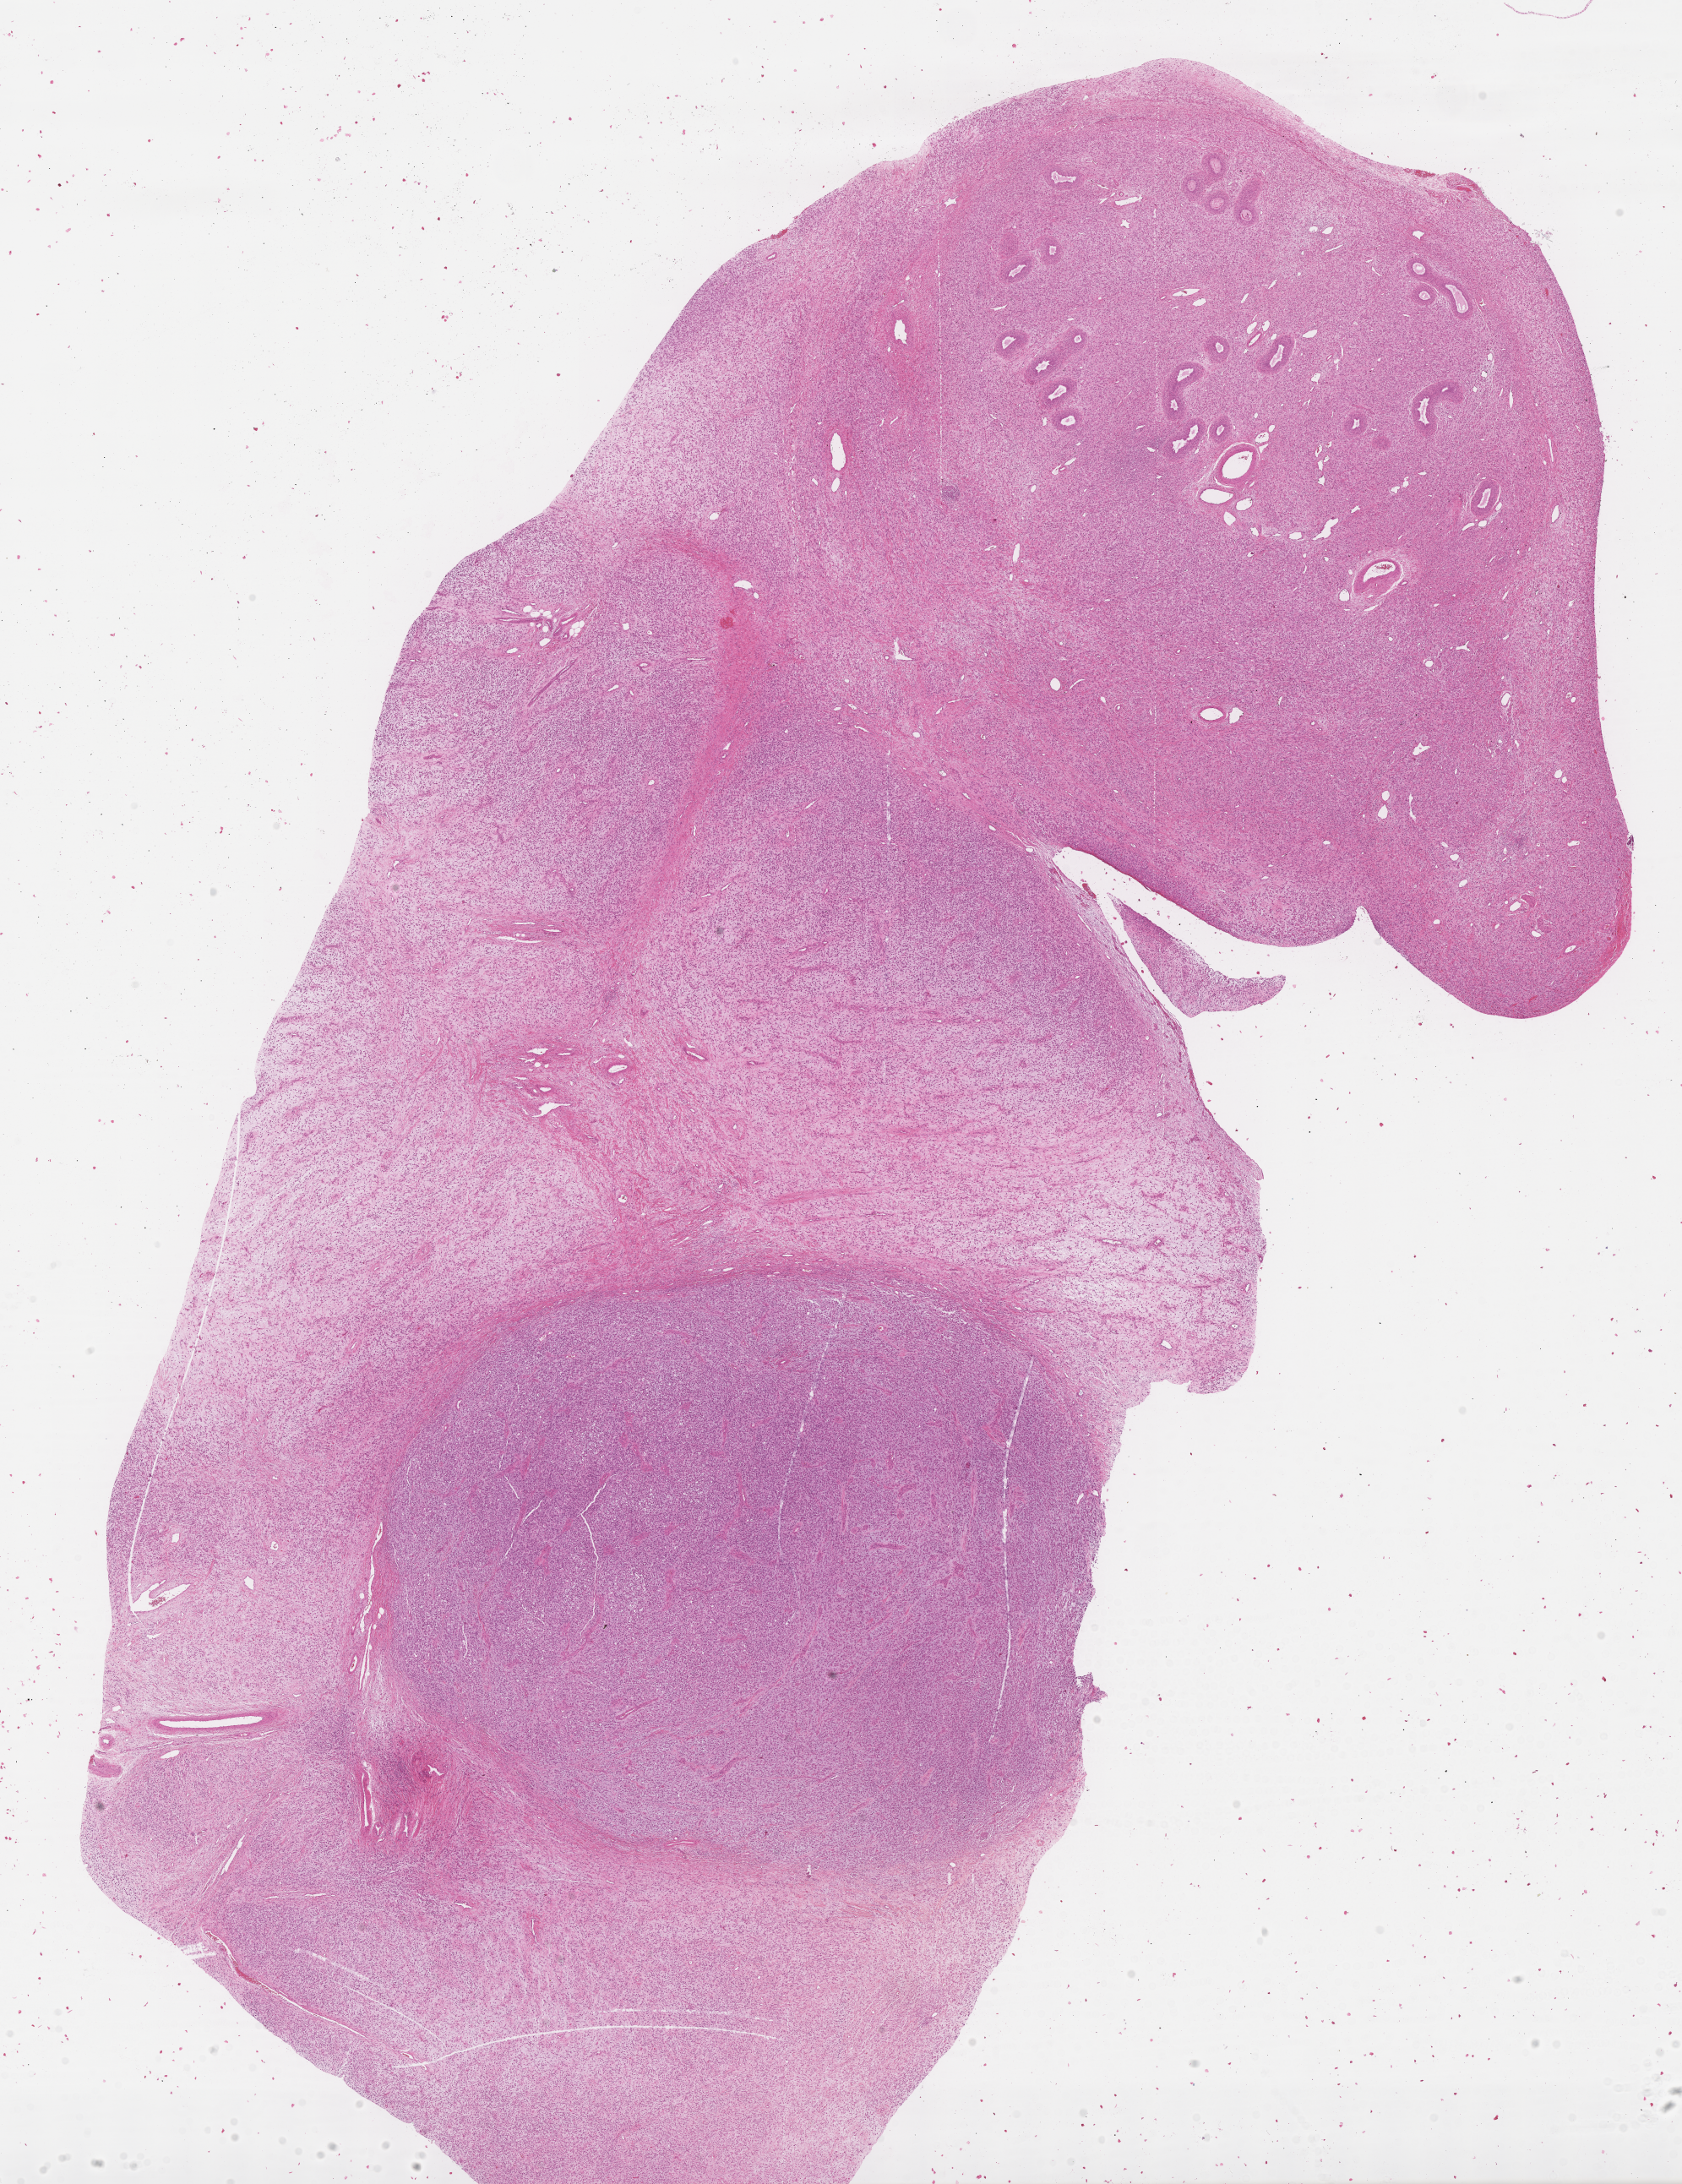
Hematoxylin and eosin (H&E) whole-slide image of tumor tissue — shown as a low-resolution overview of the whole scanned area (about 16.1 x 20.9 mm), formalin-fixed paraffin-embedded section, site: soft tissue - testicle, left. Male patient, age at diagnosis 5.2 years.
Diagnosis: rhabdomyosarcoma; histological classification: embryonal rhabdomyosarcoma.